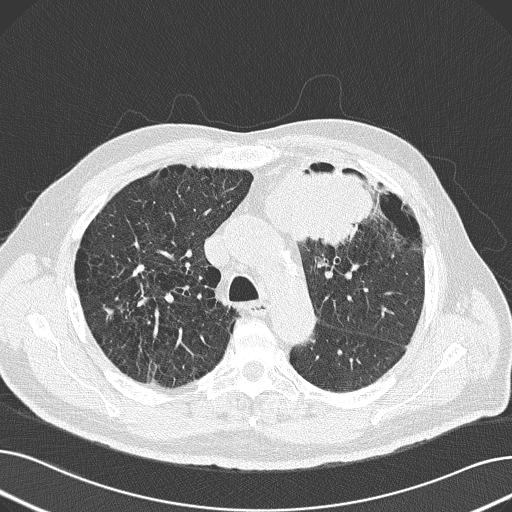
Axial slice from a low-dose chest CT screening exam; baseline screening round; lung window (W 1500 / L -600 HU); 2 mm slice thickness; slice 58 of 165 in the series; 512 × 512 image matrix. Male participant, aged 69 years at enrolment. Former smoker at enrolment.
• Lesion marked by an expert reader, bounding box (x1, y1, x2, y2) in pixels: (227, 146, 380, 254).
• Screening reader's record for this exam (one nodule recorded; not confirmed to be the boxed lesion): non-calcified nodule or mass ≥4 mm, left upper lobe, 6 × 10 mm, spiculated (stellate) margins, soft tissue attenuation.
• Official screen result: positive, change unspecified: nodule(s) >= 4 mm or enlarging nodule(s), mass(es), or other non-specific abnormalities suspicious for lung cancer.
• Lung cancer was diagnosed 20 days after this screen: non-small cell carcinoma, left upper lobe, poorly differentiated (G3), stage IB (AJCC 6th edition), 100 mm at pathology.